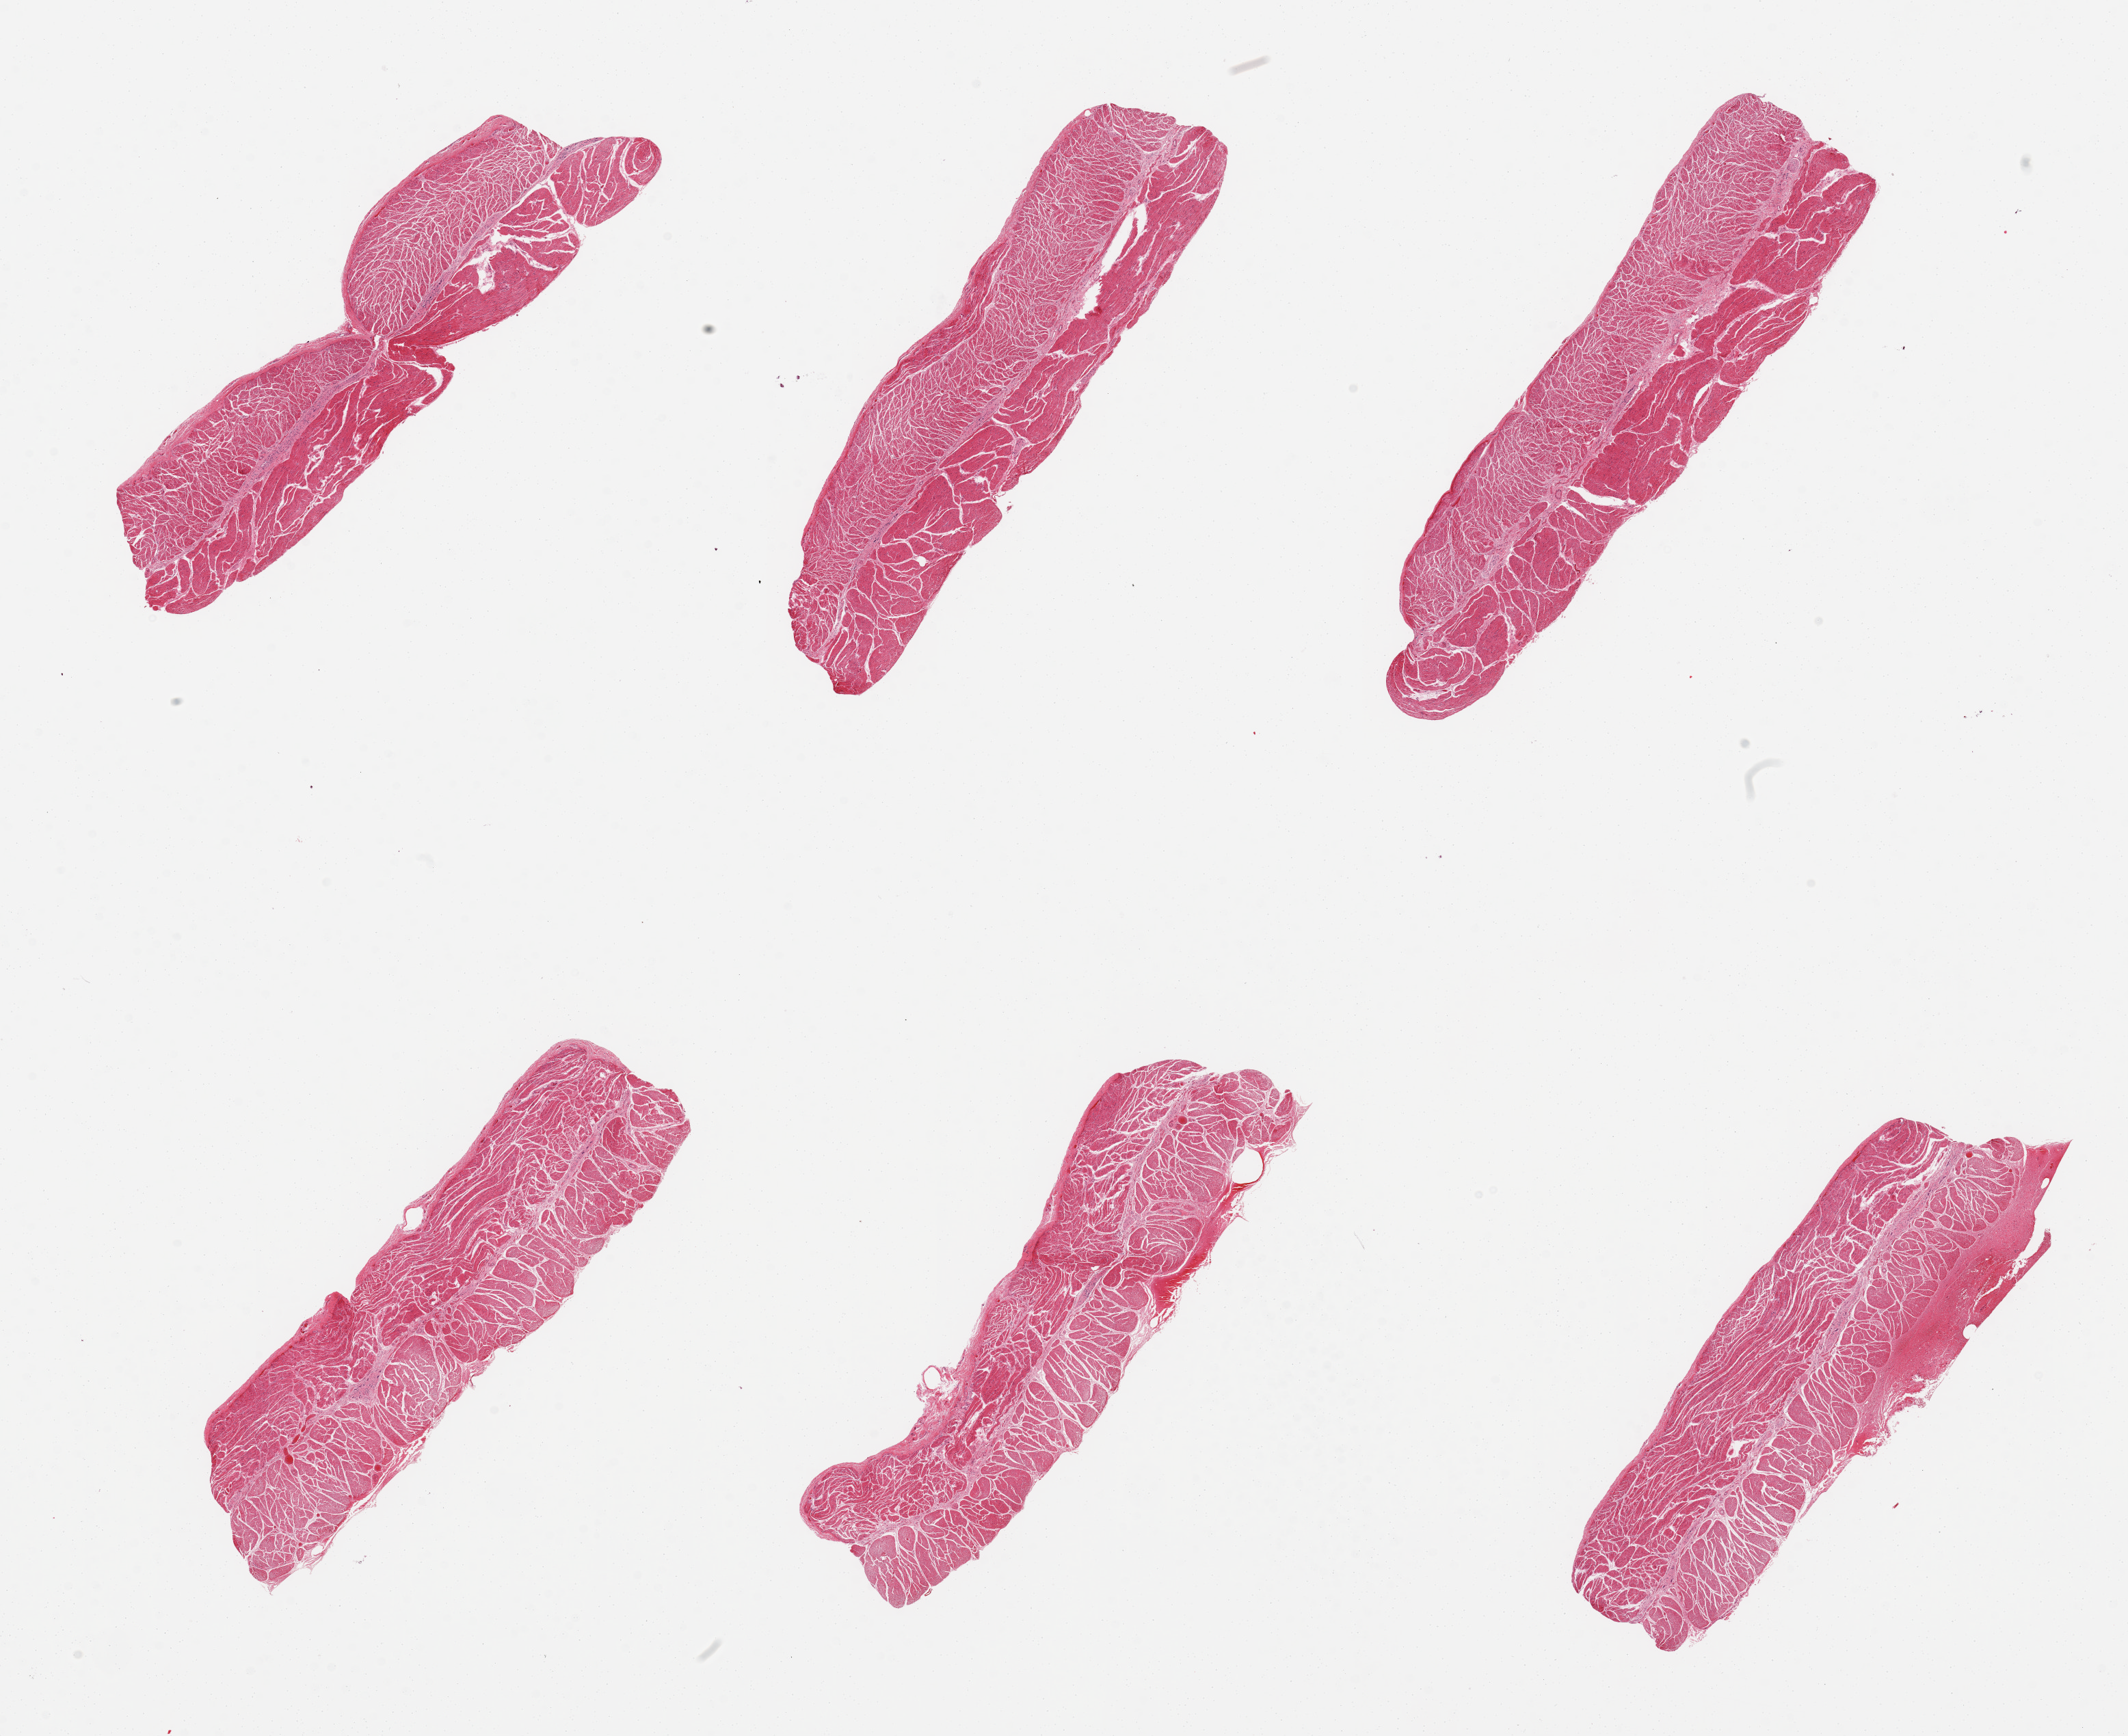
Haematoxylin and eosin whole-slide image, brightfield, low-resolution overview of the scanned area, about 24.6 x 20.1 mm (slide scanned at 20x); PAXgene-fixed, paraffin-embedded tissue; section of esophageal muscle (target tissue); donor tissue sample. Male donor.
* pathologist's review note for this sample: 6 pieces, well trimmed